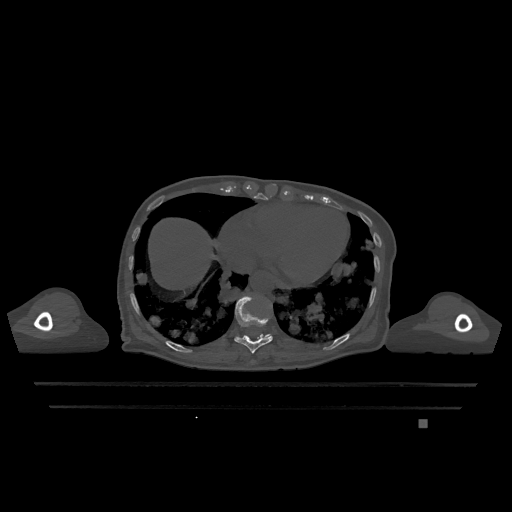
CT including the spine, one axial slice; position 631 of 1317 along the scan axis; bone window (W 1800 / L 400 HU); 512 × 512 image matrix. Female patient, age 74 years. Case-level facts recorded for this patient, not image findings: primary cancer: lung; vertebrae with lytic lesions (as recorded): T1, T4, T5, T6, L4, L5.
Annotated regions visible in this slice (semi-automatically segmented with operator editing):
- T10 vertebra: bounding box <234,296,273,353> (left, top, right, bottom; pixels)
- T11 vertebra: <268,334,270,336>